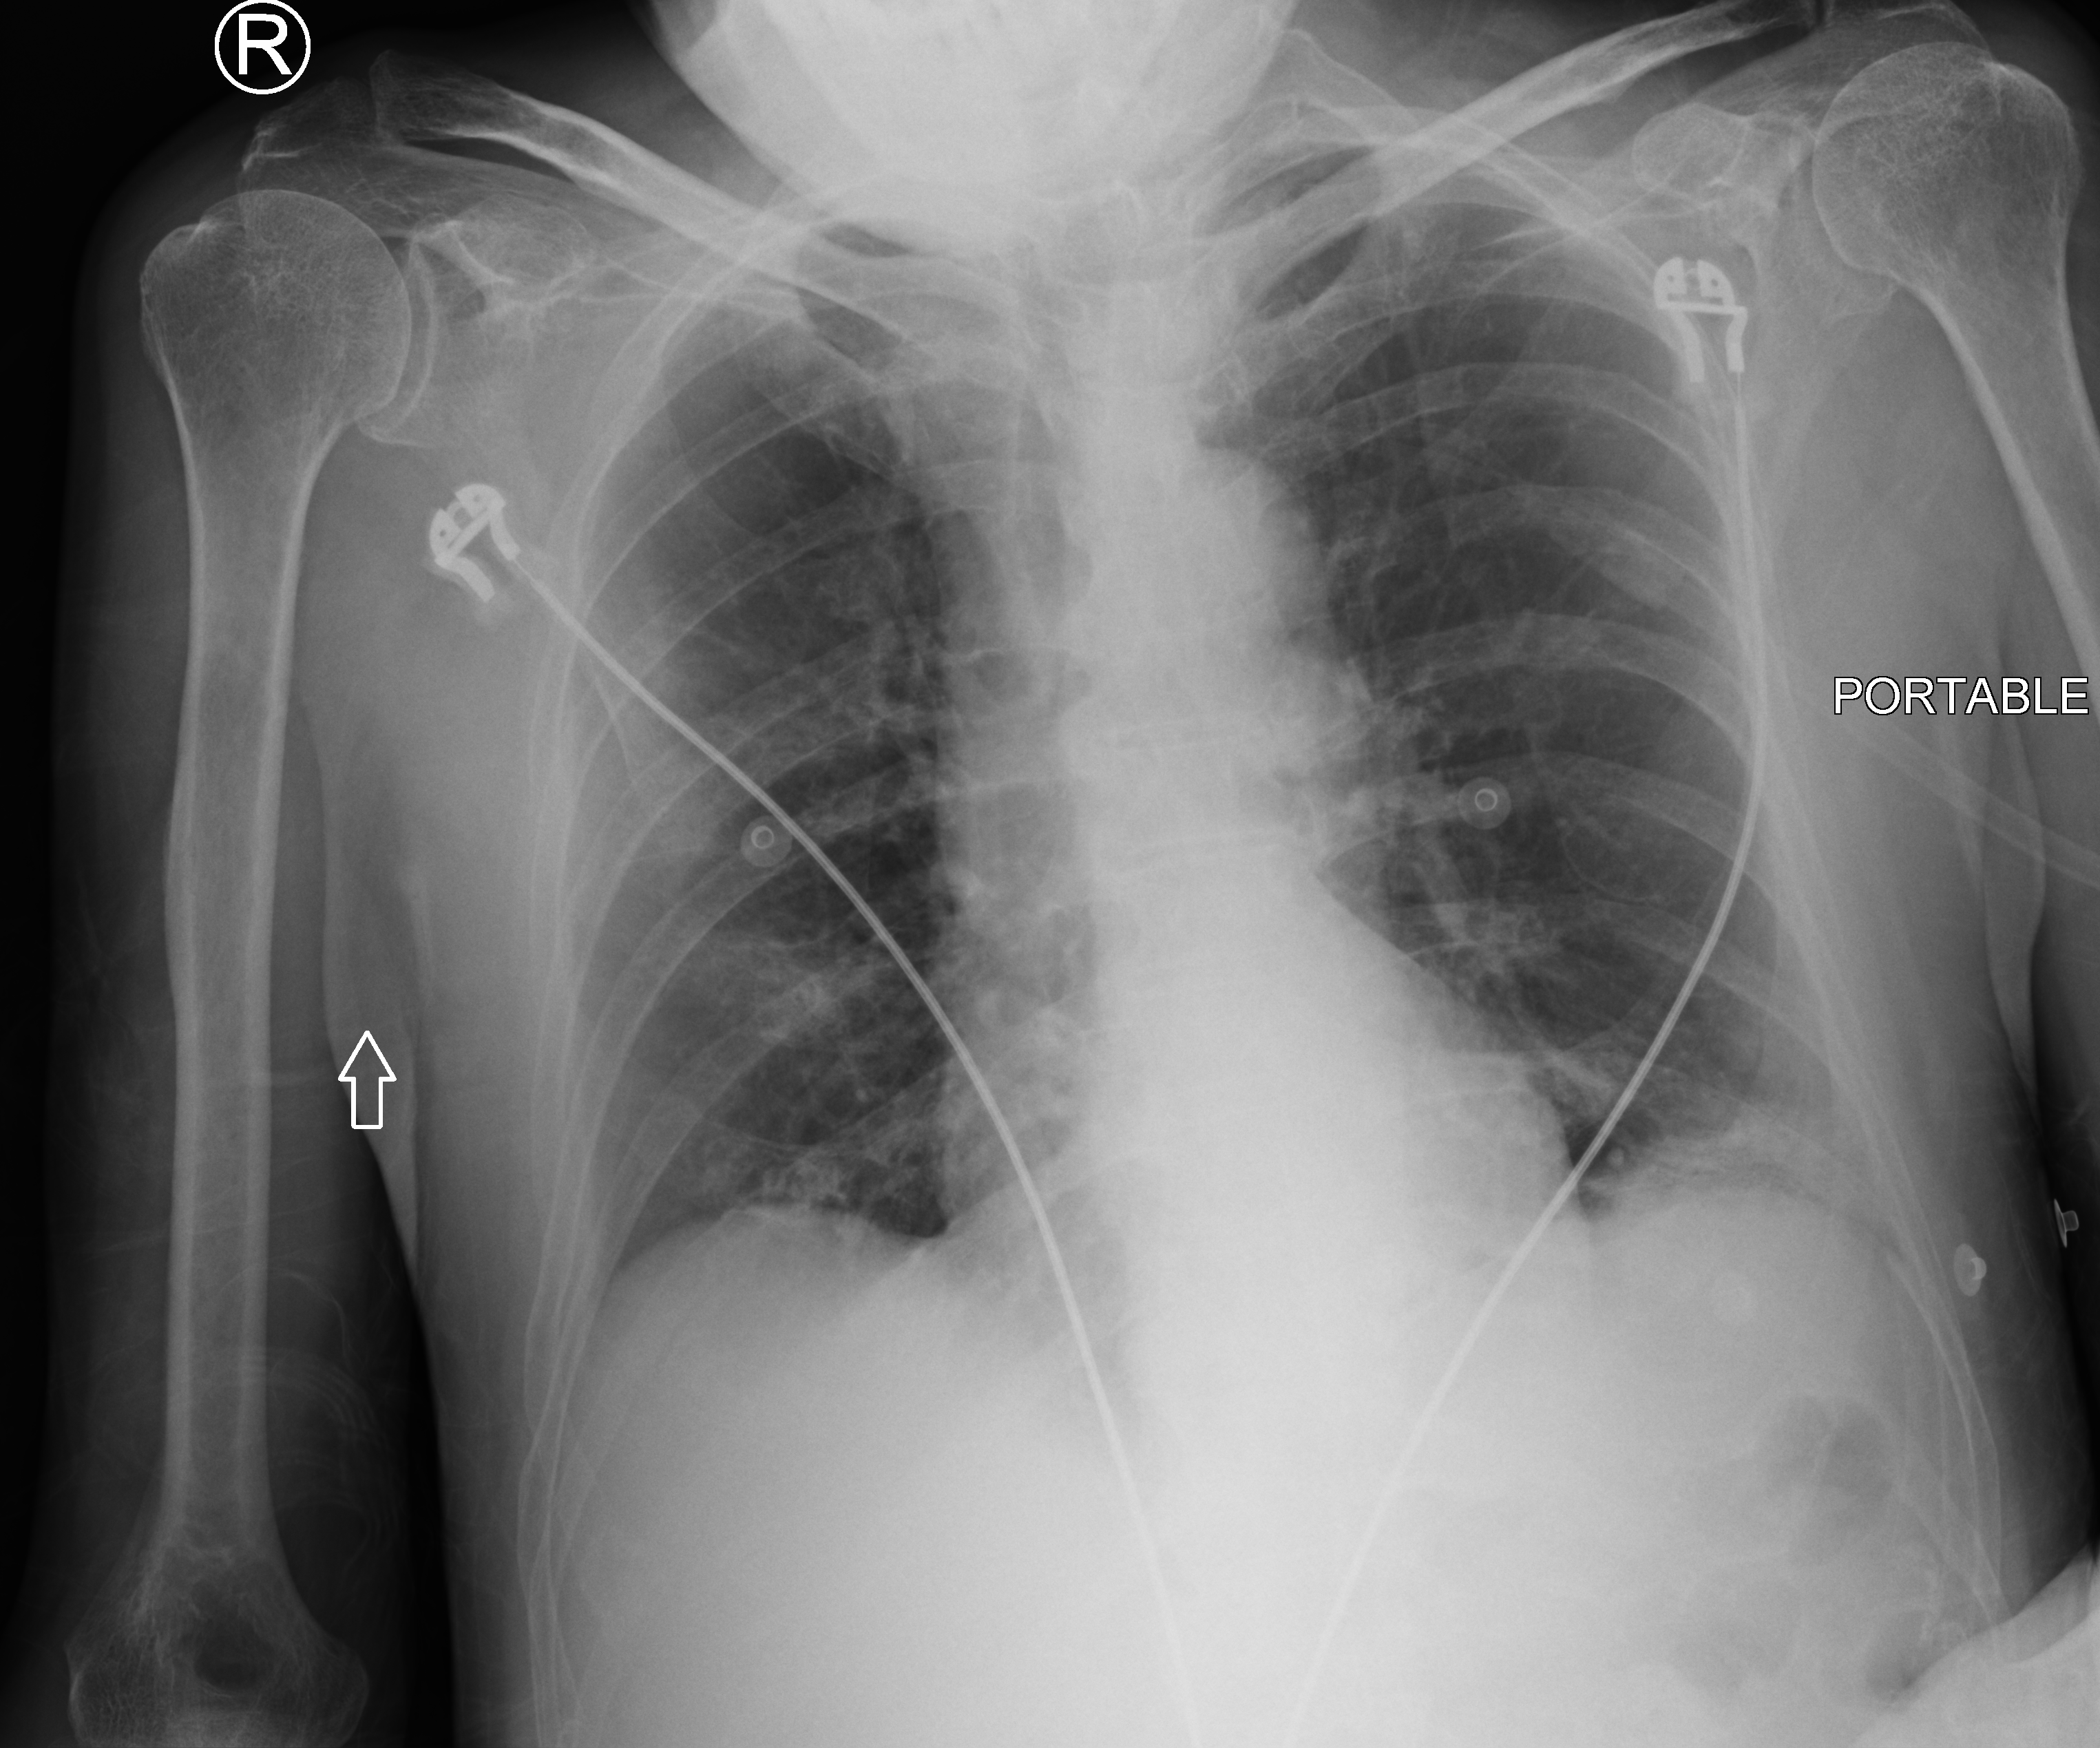
Bedside chest radiograph (computed radiography). Male patient hospitalised with COVID-19, age 60–74 years.
From the hospital-stay record, not from the radiograph (when in the stay this image was taken is not recorded): smoking status (admission record): current; admitted to intensive care during this hospital stay: yes; mechanically ventilated during this hospital stay: yes.